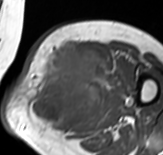
MRI of an extremity soft-tissue mass, one axial slice; slice 41 of 65 in the series (ordered by position); MR volume resampled by the dataset authors to the PET/CT grid (not the native acquisition matrix); 3.27 mm slice thickness; 163 × 155 image matrix, field of view 159 × 151 mm. Female patient. From the clinical record (not read from this slice): histological type: pleomorphic leiomyosarcoma; grade: high; site of the primary tumour: left thigh.
Outlined on this slice (expert contour drawn on MRI and transferred to this co-registered scan by the dataset authors):
- gross tumour volume including surrounding oedema: bounding box <30,42,107,132> (left, top, right, bottom; pixels)
- gross tumour volume (mass): <39,42,100,121>